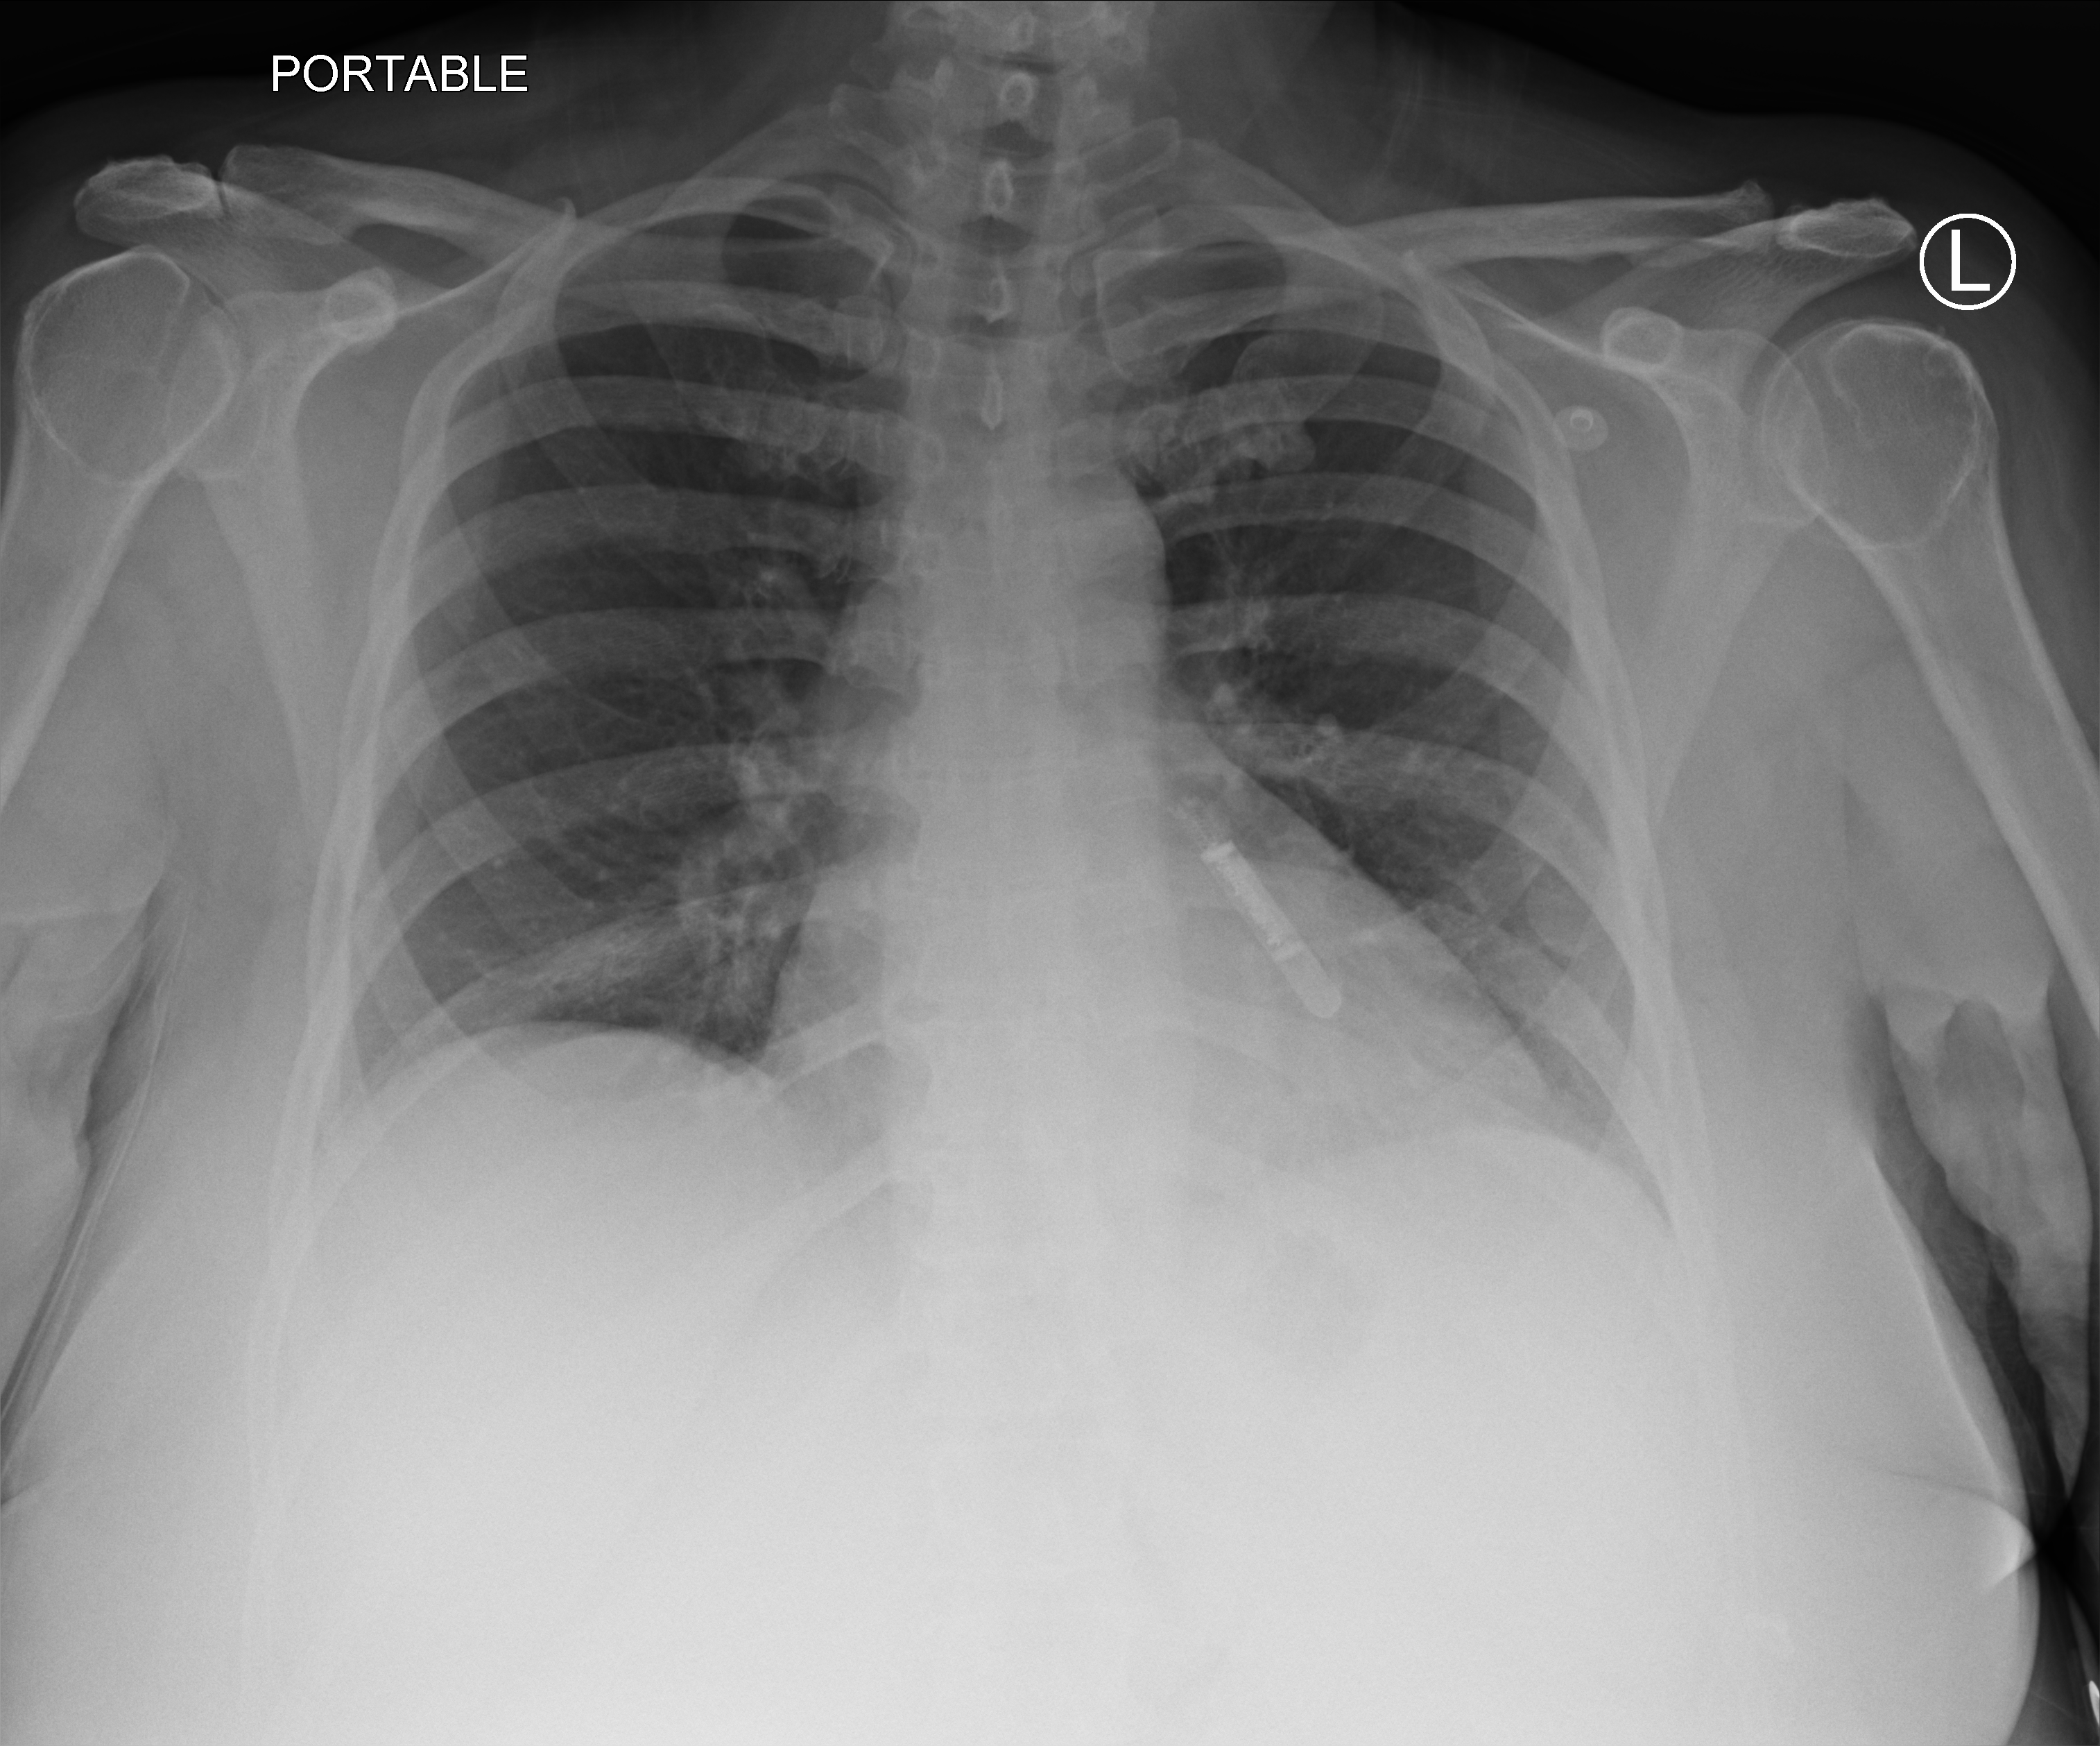
Bedside chest radiograph (computed radiography); anteroposterior (AP) projection. Patient hospitalised with COVID-19; female, aged 18–59 years.
From the hospital-stay record, not from the radiograph (when in the stay this image was taken is not recorded):
- mechanically ventilated during this hospital stay: no
- admitted to intensive care during this hospital stay: no
- COPD (admission record): no